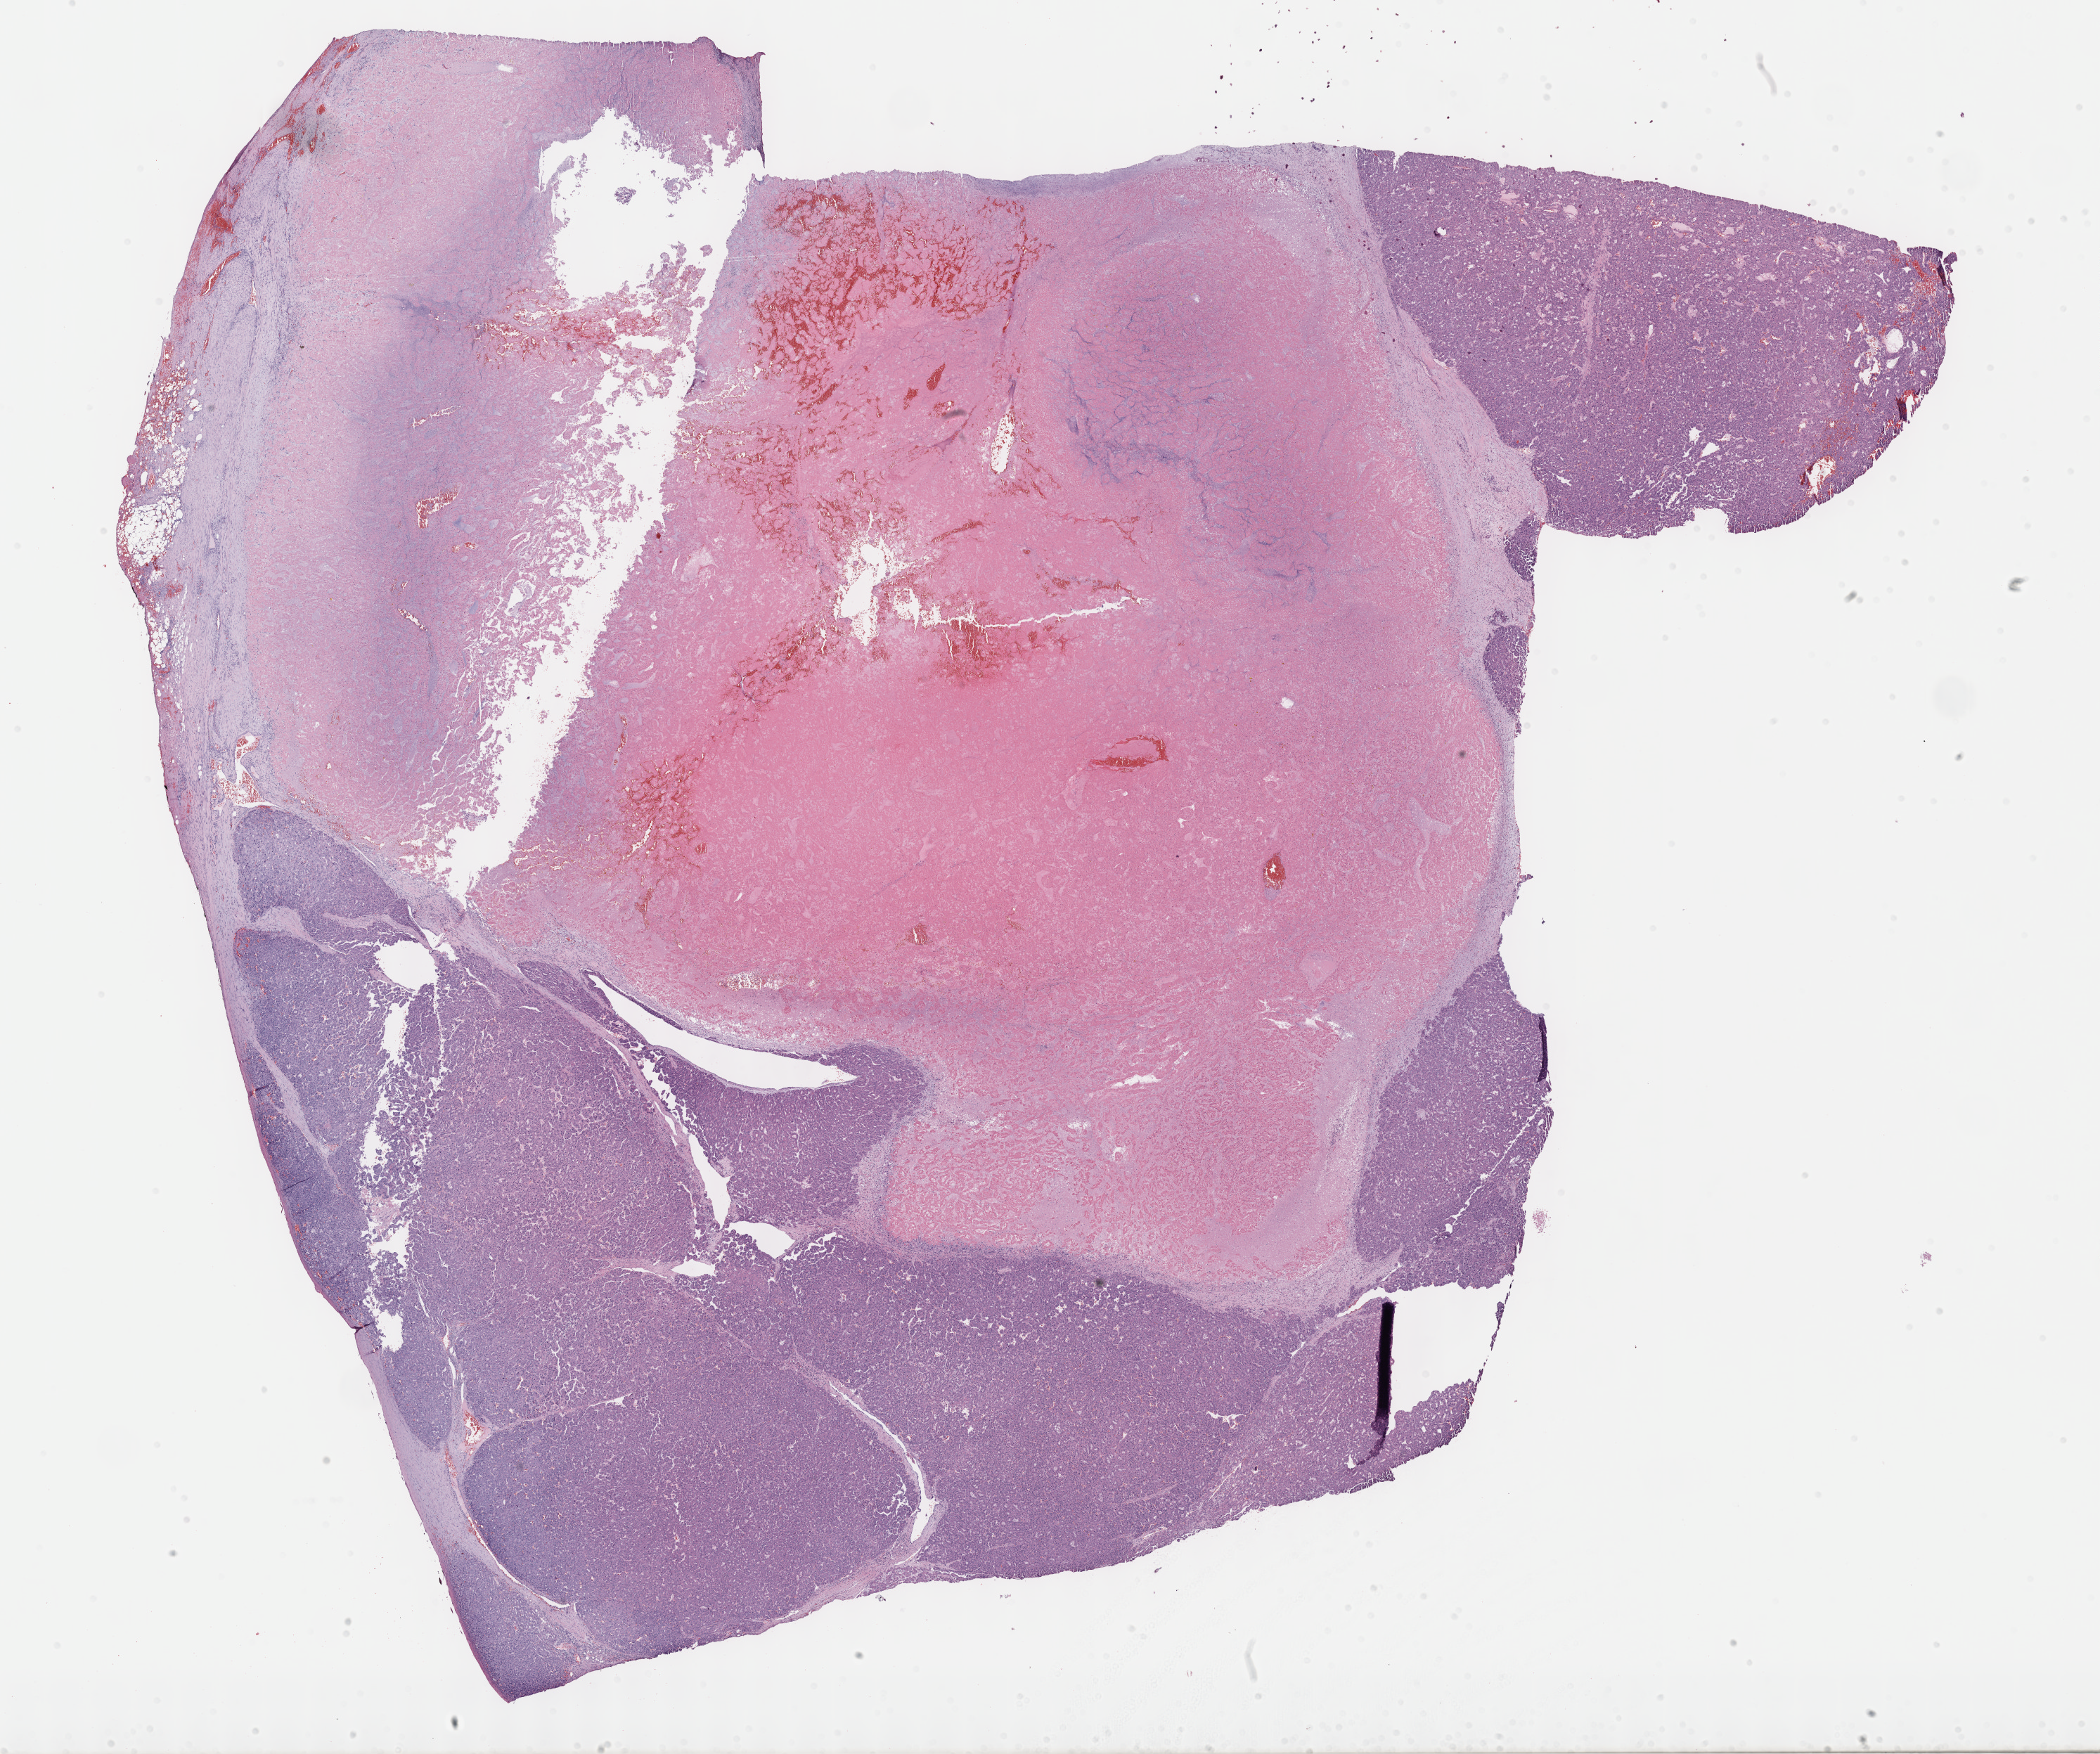
H&E-stained whole-slide image, low-resolution overview of the scanned area, about 24.2 x 20.2 mm (acquisition: 40x scan); FFPE section; primary tumour sample from the liver. Female, age 33 years at initial diagnosis. Histologic grade: G2 (moderately differentiated).
• pathologic diagnosis: Hepatocellular carcinoma, NOS
• AJCC pathologic stage: IIIA (7th edition)
• TNM: T3a NX MX